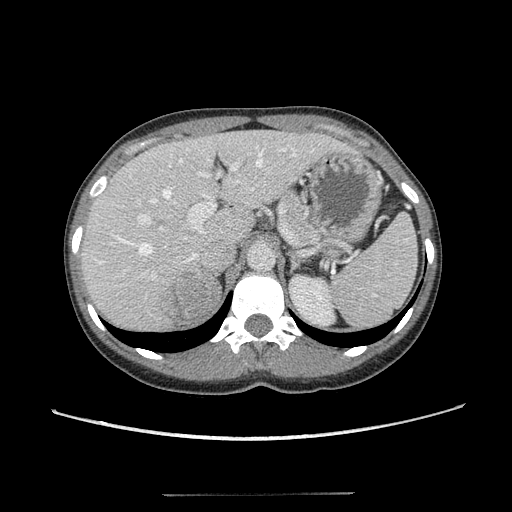
Contrast-enhanced abdominal CT, one axial slice. Position 80 of 117 along the scan axis. Reconstruction kernel STANDARD. Intravenous contrast given. Soft-tissue window (W 400 / L 40 HU). 512 × 512 image matrix, field of view 365 × 365 mm. Patient: female, 35 years. Case-level facts recorded for this patient, not image findings: diagnosis: adrenocortical carcinoma; tumour side: right adrenal; tumour size at pathology: 3 cm; Ki-67 index: 21 %; stage (as recorded): 3.
Outlined on this slice (semi-automatically segmented with operator editing):
- mass: box from (x=162, y=273) to (x=216, y=324) px